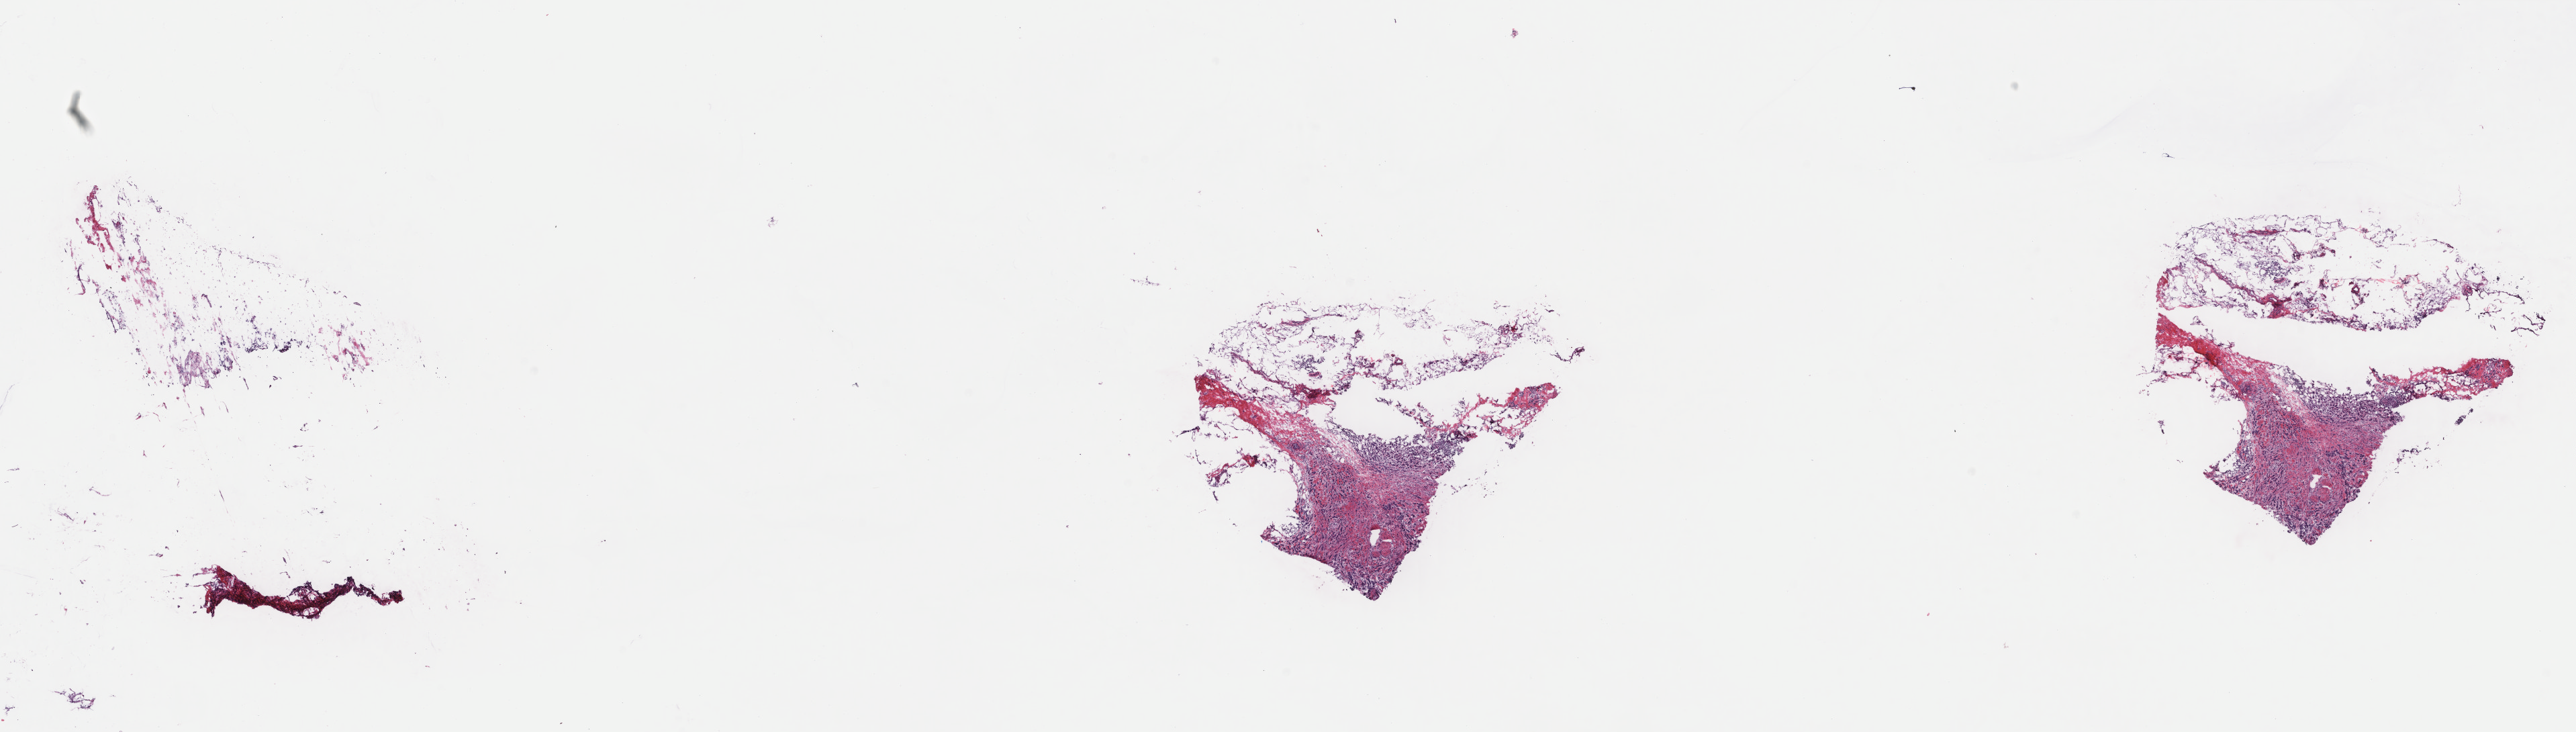
Whole-slide histology image, Hematoxylin and eosin (H&E) stained — a low-resolution overview of the entire scanned area, about 30.5 x 8.7 mm (from a 40x scan). Frozen section from the top of the tissue portion. Sample: primary tumour, breast. Female patient; age at initial diagnosis 53 years. Slide review estimates, as recorded: tumour cells 40%, tumour nuclei 60%, normal cells 0%, stromal cells 60%, necrosis 0%. Infiltration values recorded for this section: lymphocyte infiltration 0%, monocyte infiltration 0%, neutrophil infiltration 0%.
• lymph nodes positive (case pathology): 12 of 12 examined
• pathologic diagnosis: Lobular carcinoma, NOS
• AJCC pathologic stage: IIIC (7th edition)